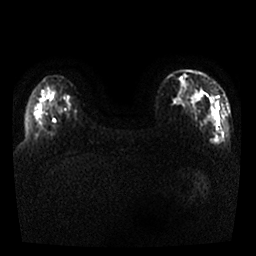
Breast MRI, one axial slice; position 5 of 25 along the scan axis; diffusion-weighted series; image 2 of 4 stored at this slice position (different b-values; order by instance number); 1.5 T; 4 mm slice thickness; 256 × 256 image matrix, field of view 340 × 340 mm. Female patient.
Structures marked on this image (manually delineated by an expert):
- tumour on diffusion-weighted imaging: bounding box [x1, y1, x2, y2] px = [173, 89, 225, 142]